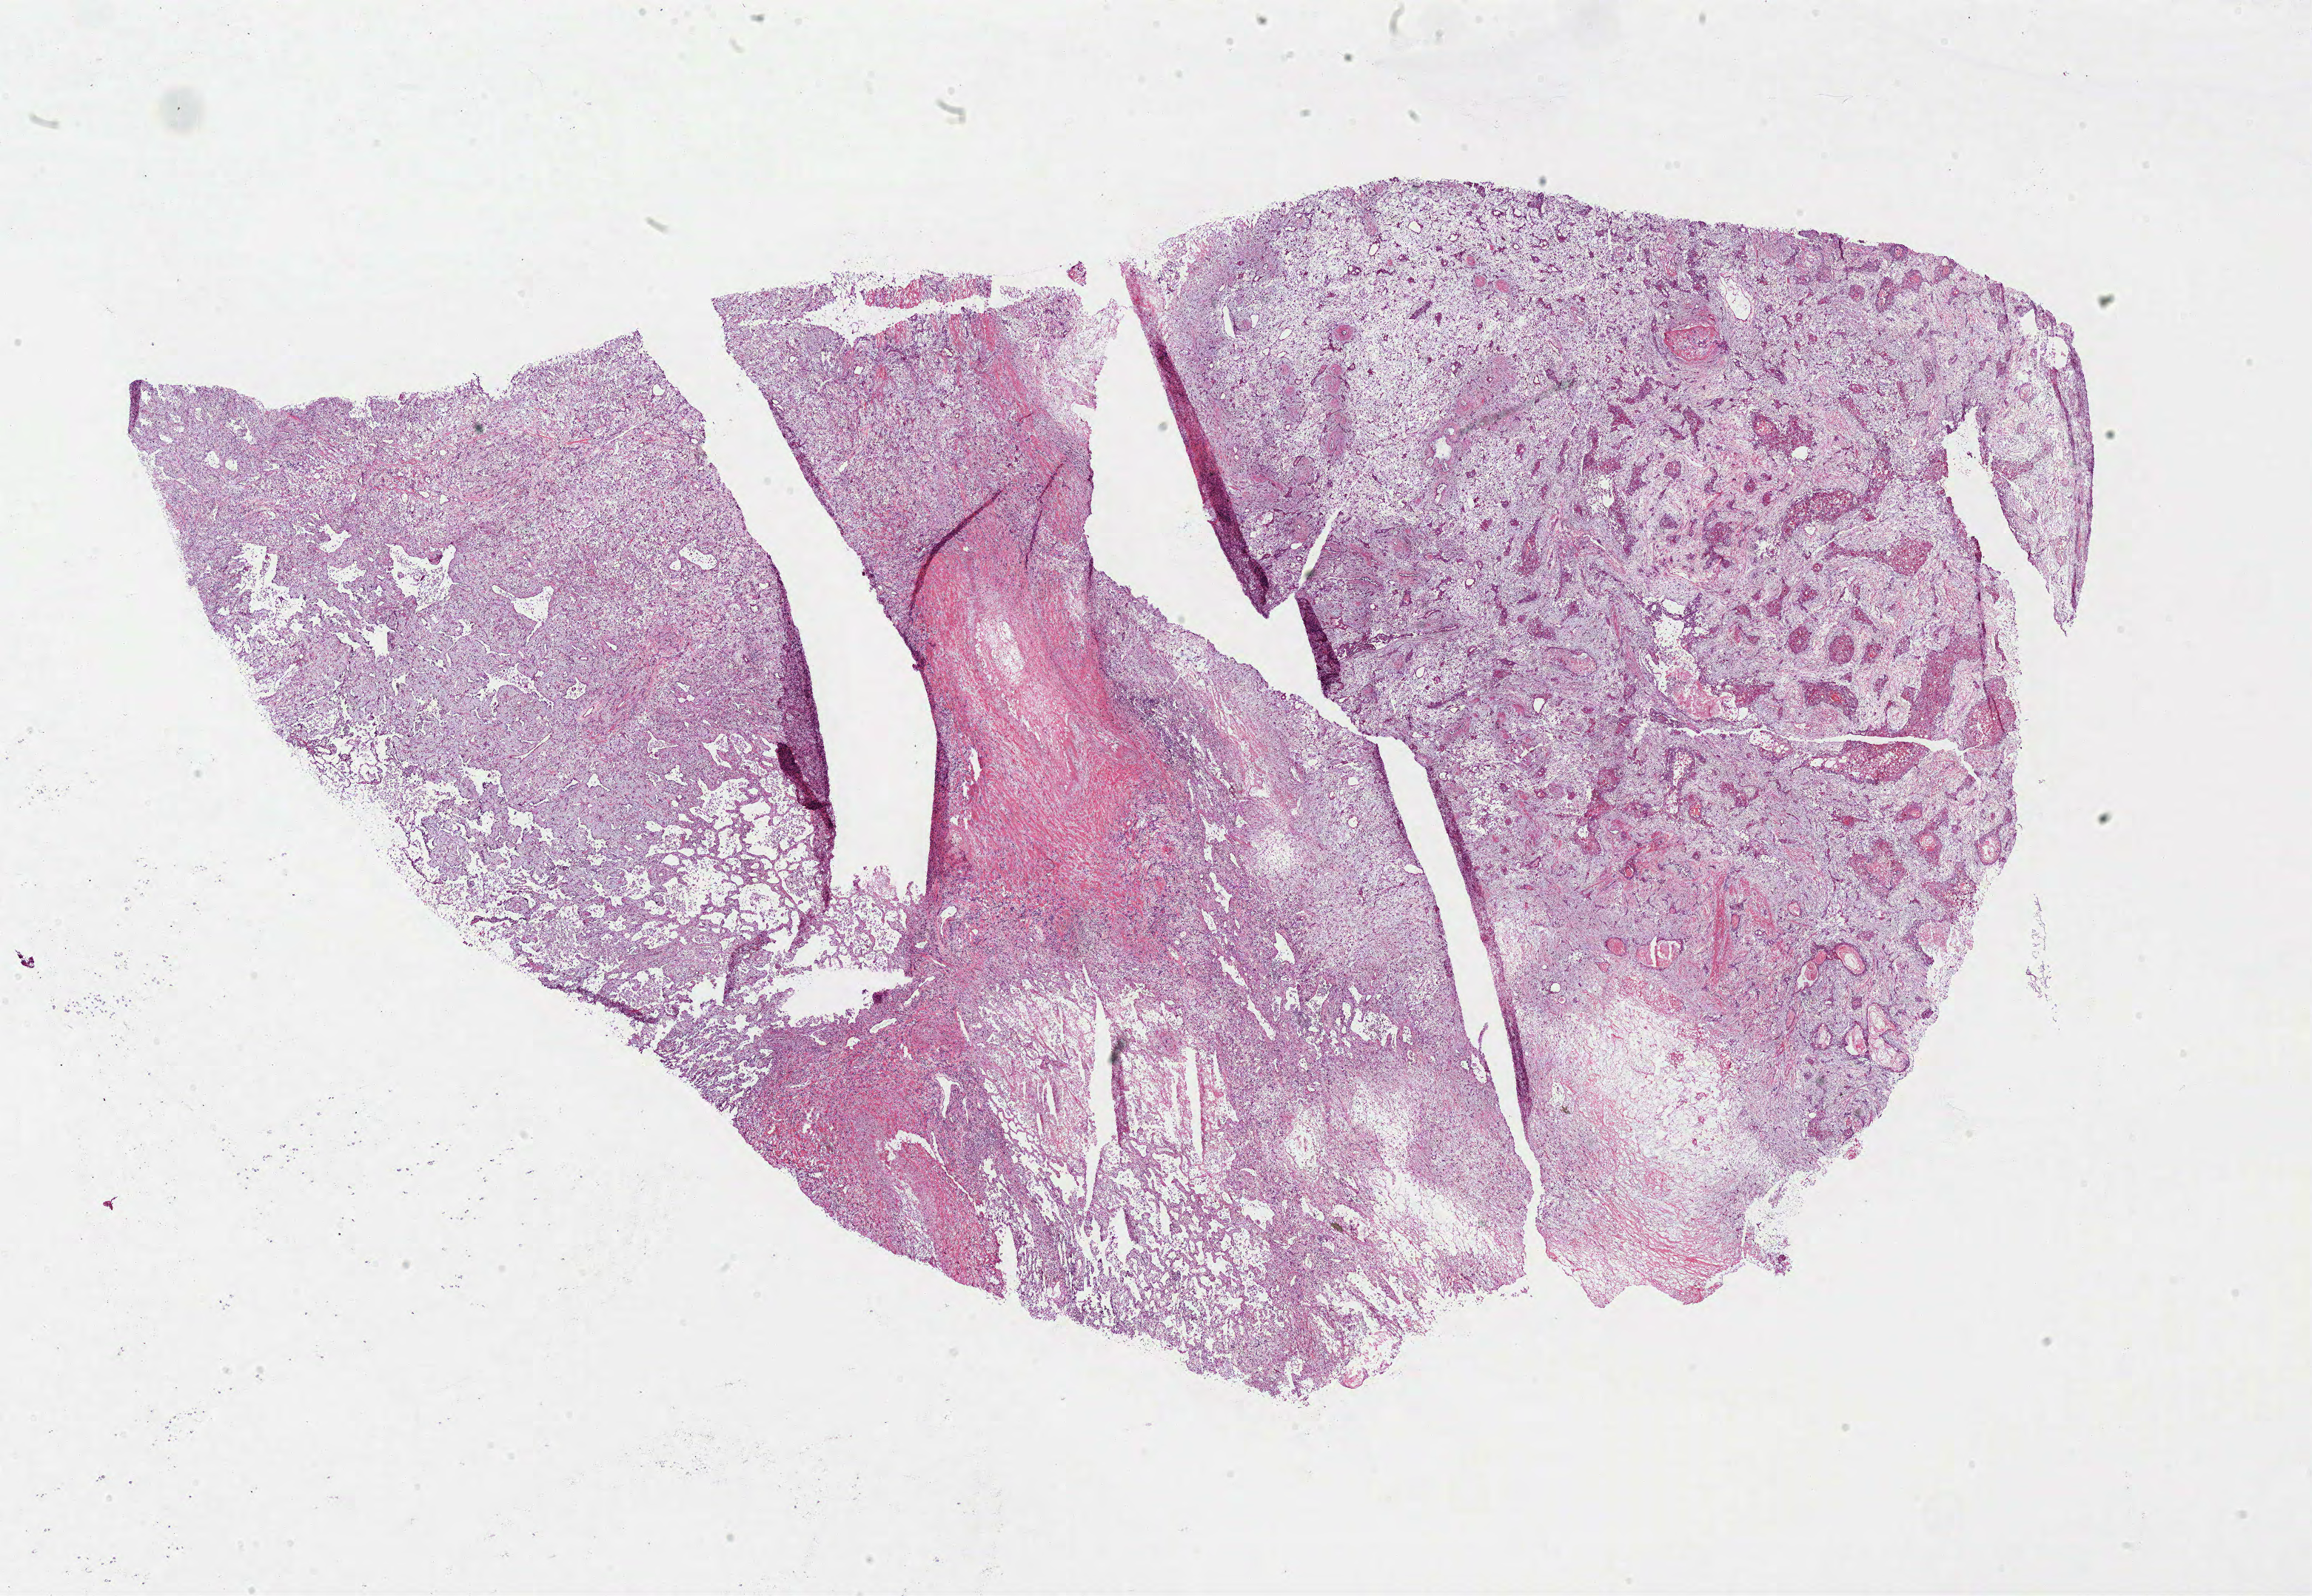
Whole-slide histology image, H&E — low-resolution overview of the scanned area, about 24.6 x 17.0 mm (from a 40x scan), frozen section, lung, primary tumour sample. Female patient; age at initial diagnosis 63 years. Pathologist review of this section (percent, as recorded): tumour cells 52%, tumour nuclei 70%, normal cells 20%, stromal cells 25%, necrosis 3%.
• TNM: T3 N0 M0
• pathologic diagnosis: Squamous cell carcinoma, NOS (upper lobe, lung)
• AJCC pathologic stage: IIB (7th edition)